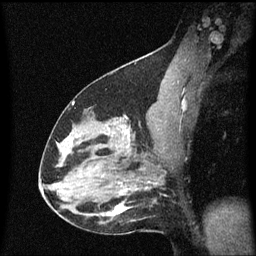
Breast MRI (dynamic contrast-enhanced), one sagittal slice. Position 35 of 60 along the scan axis. Dynamic contrast-enhanced series, image 2 of 3 at this slice position (ordered by acquisition). 1.5 T. TE 4.2 ms, TR 8.4 ms. 256 × 256 image matrix, field of view 200 × 200 mm. Patient: female, 38 years. From the clinical record (not read from this slice): setting: breast cancer imaged before/during neoadjuvant chemotherapy; receptor status: HR-positive, HER2-negative.
Structures marked on this image (semi-automatic segmentation, software-assisted and operator-edited):
- analysis volume of interest (the breast-tissue region the enhancement analysis was run in; not a lesion): bounding box [x1, y1, x2, y2] px = [122, 126, 154, 163]
- tumour enhancement mask (voxels above the 70 % enhancement threshold inside the analysis volume of interest): [126, 126, 131, 149]